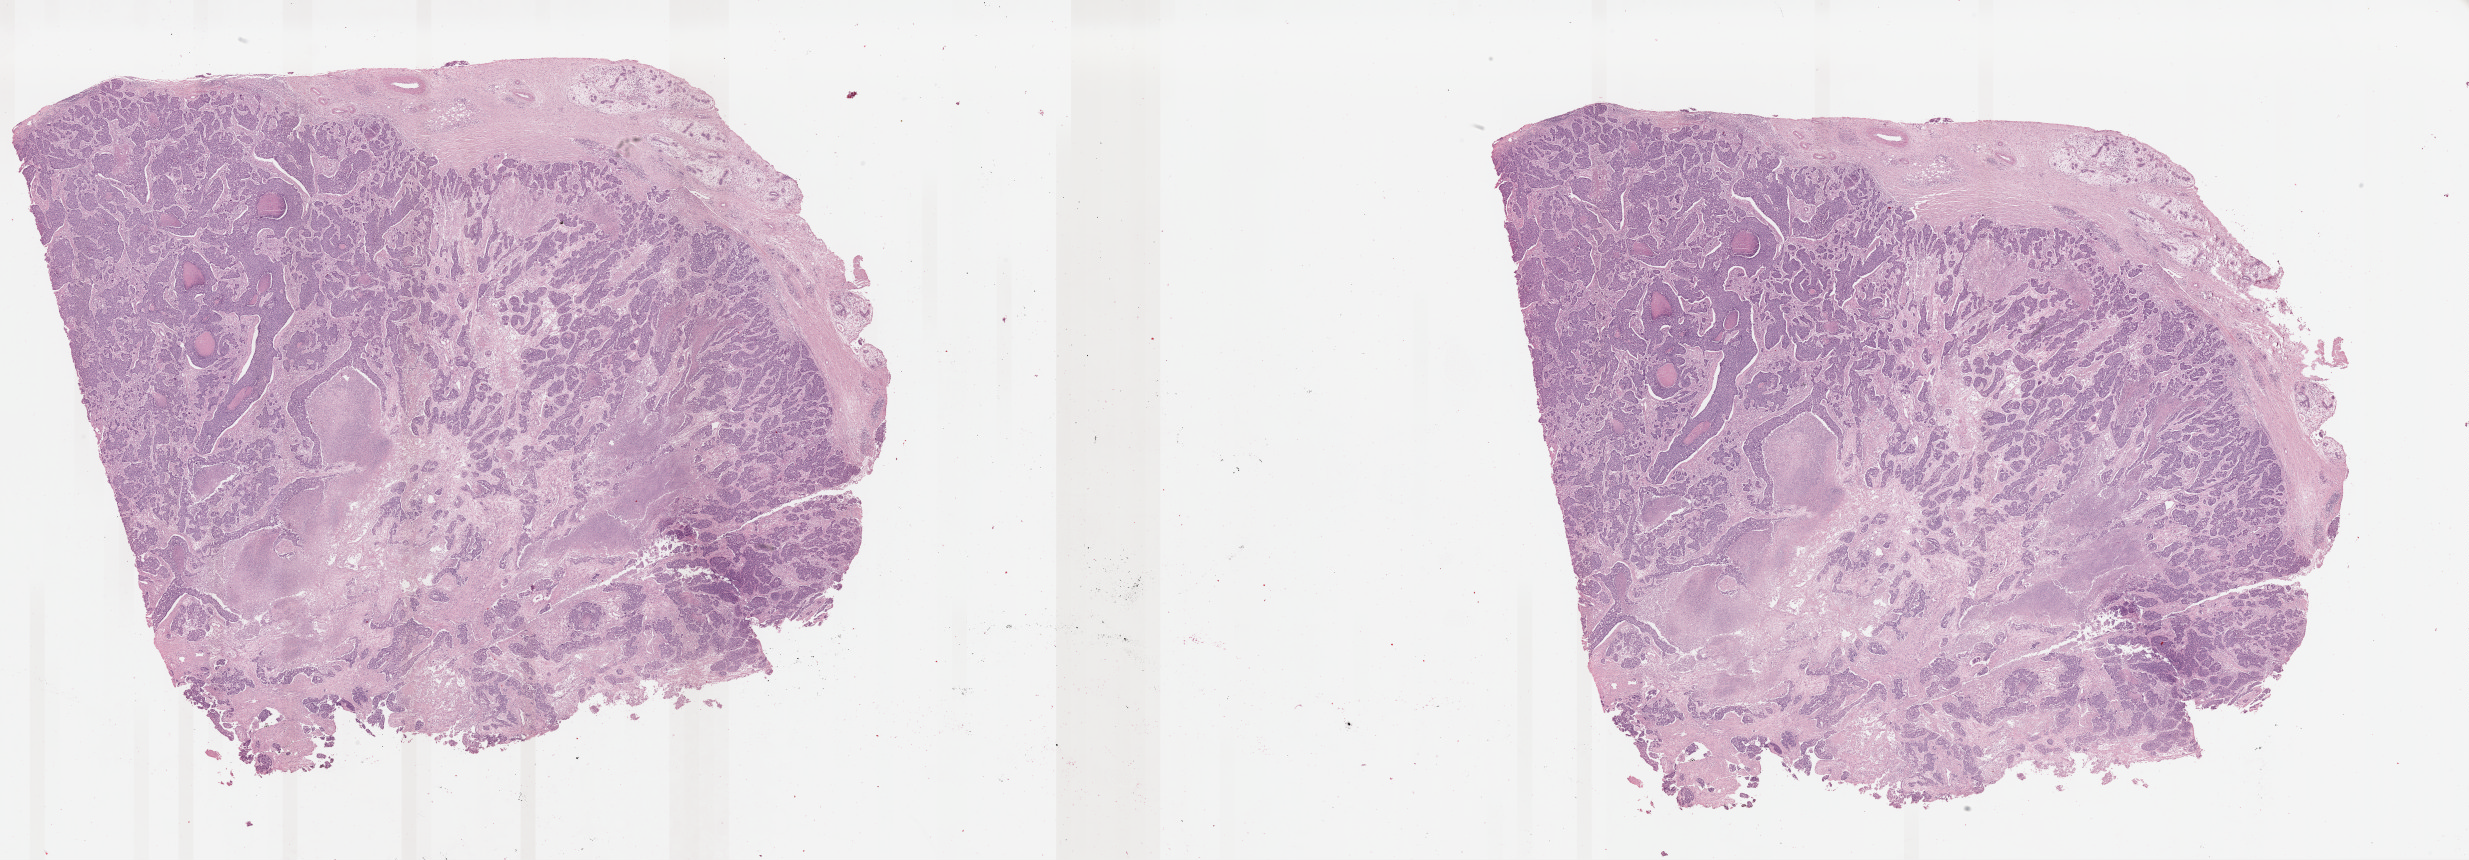
Whole-slide histology image, H&E — whole scanned area (about 39.0 x 13.6 mm) shown as a low-resolution overview. Formalin-fixed paraffin-embedded (FFPE) diagnostic section. Breast, primary tumour sample. Patient: female, age at initial diagnosis 40 years.
Lymph nodes positive (case pathology): 0 of 11 examined. Histologic diagnosis: Infiltrating duct carcinoma, NOS. AJCC pathologic stage: IIA (7th edition).